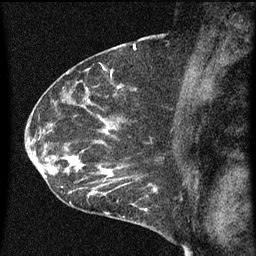
Breast MRI (dynamic contrast-enhanced), one sagittal slice; position 40 of 60 along the scan axis; dynamic contrast-enhanced series, image 2 of 3 at this slice position (ordered by acquisition); 1.5 T; TE 4.2 ms, TR 8 ms; 2 mm slice thickness; 256 × 256 image matrix, field of view 180 × 180 mm. Patient: female, 54 years.
Outlined on this slice (semi-automatically segmented with operator editing):
- analysis volume of interest (the breast-tissue region the enhancement analysis was run in; not a lesion): bounding box (x1, y1, x2, y2) in pixels: (49, 138, 163, 209)
- tumour enhancement mask (voxels above the 70 % enhancement threshold inside the analysis volume of interest): (49, 140, 158, 209)